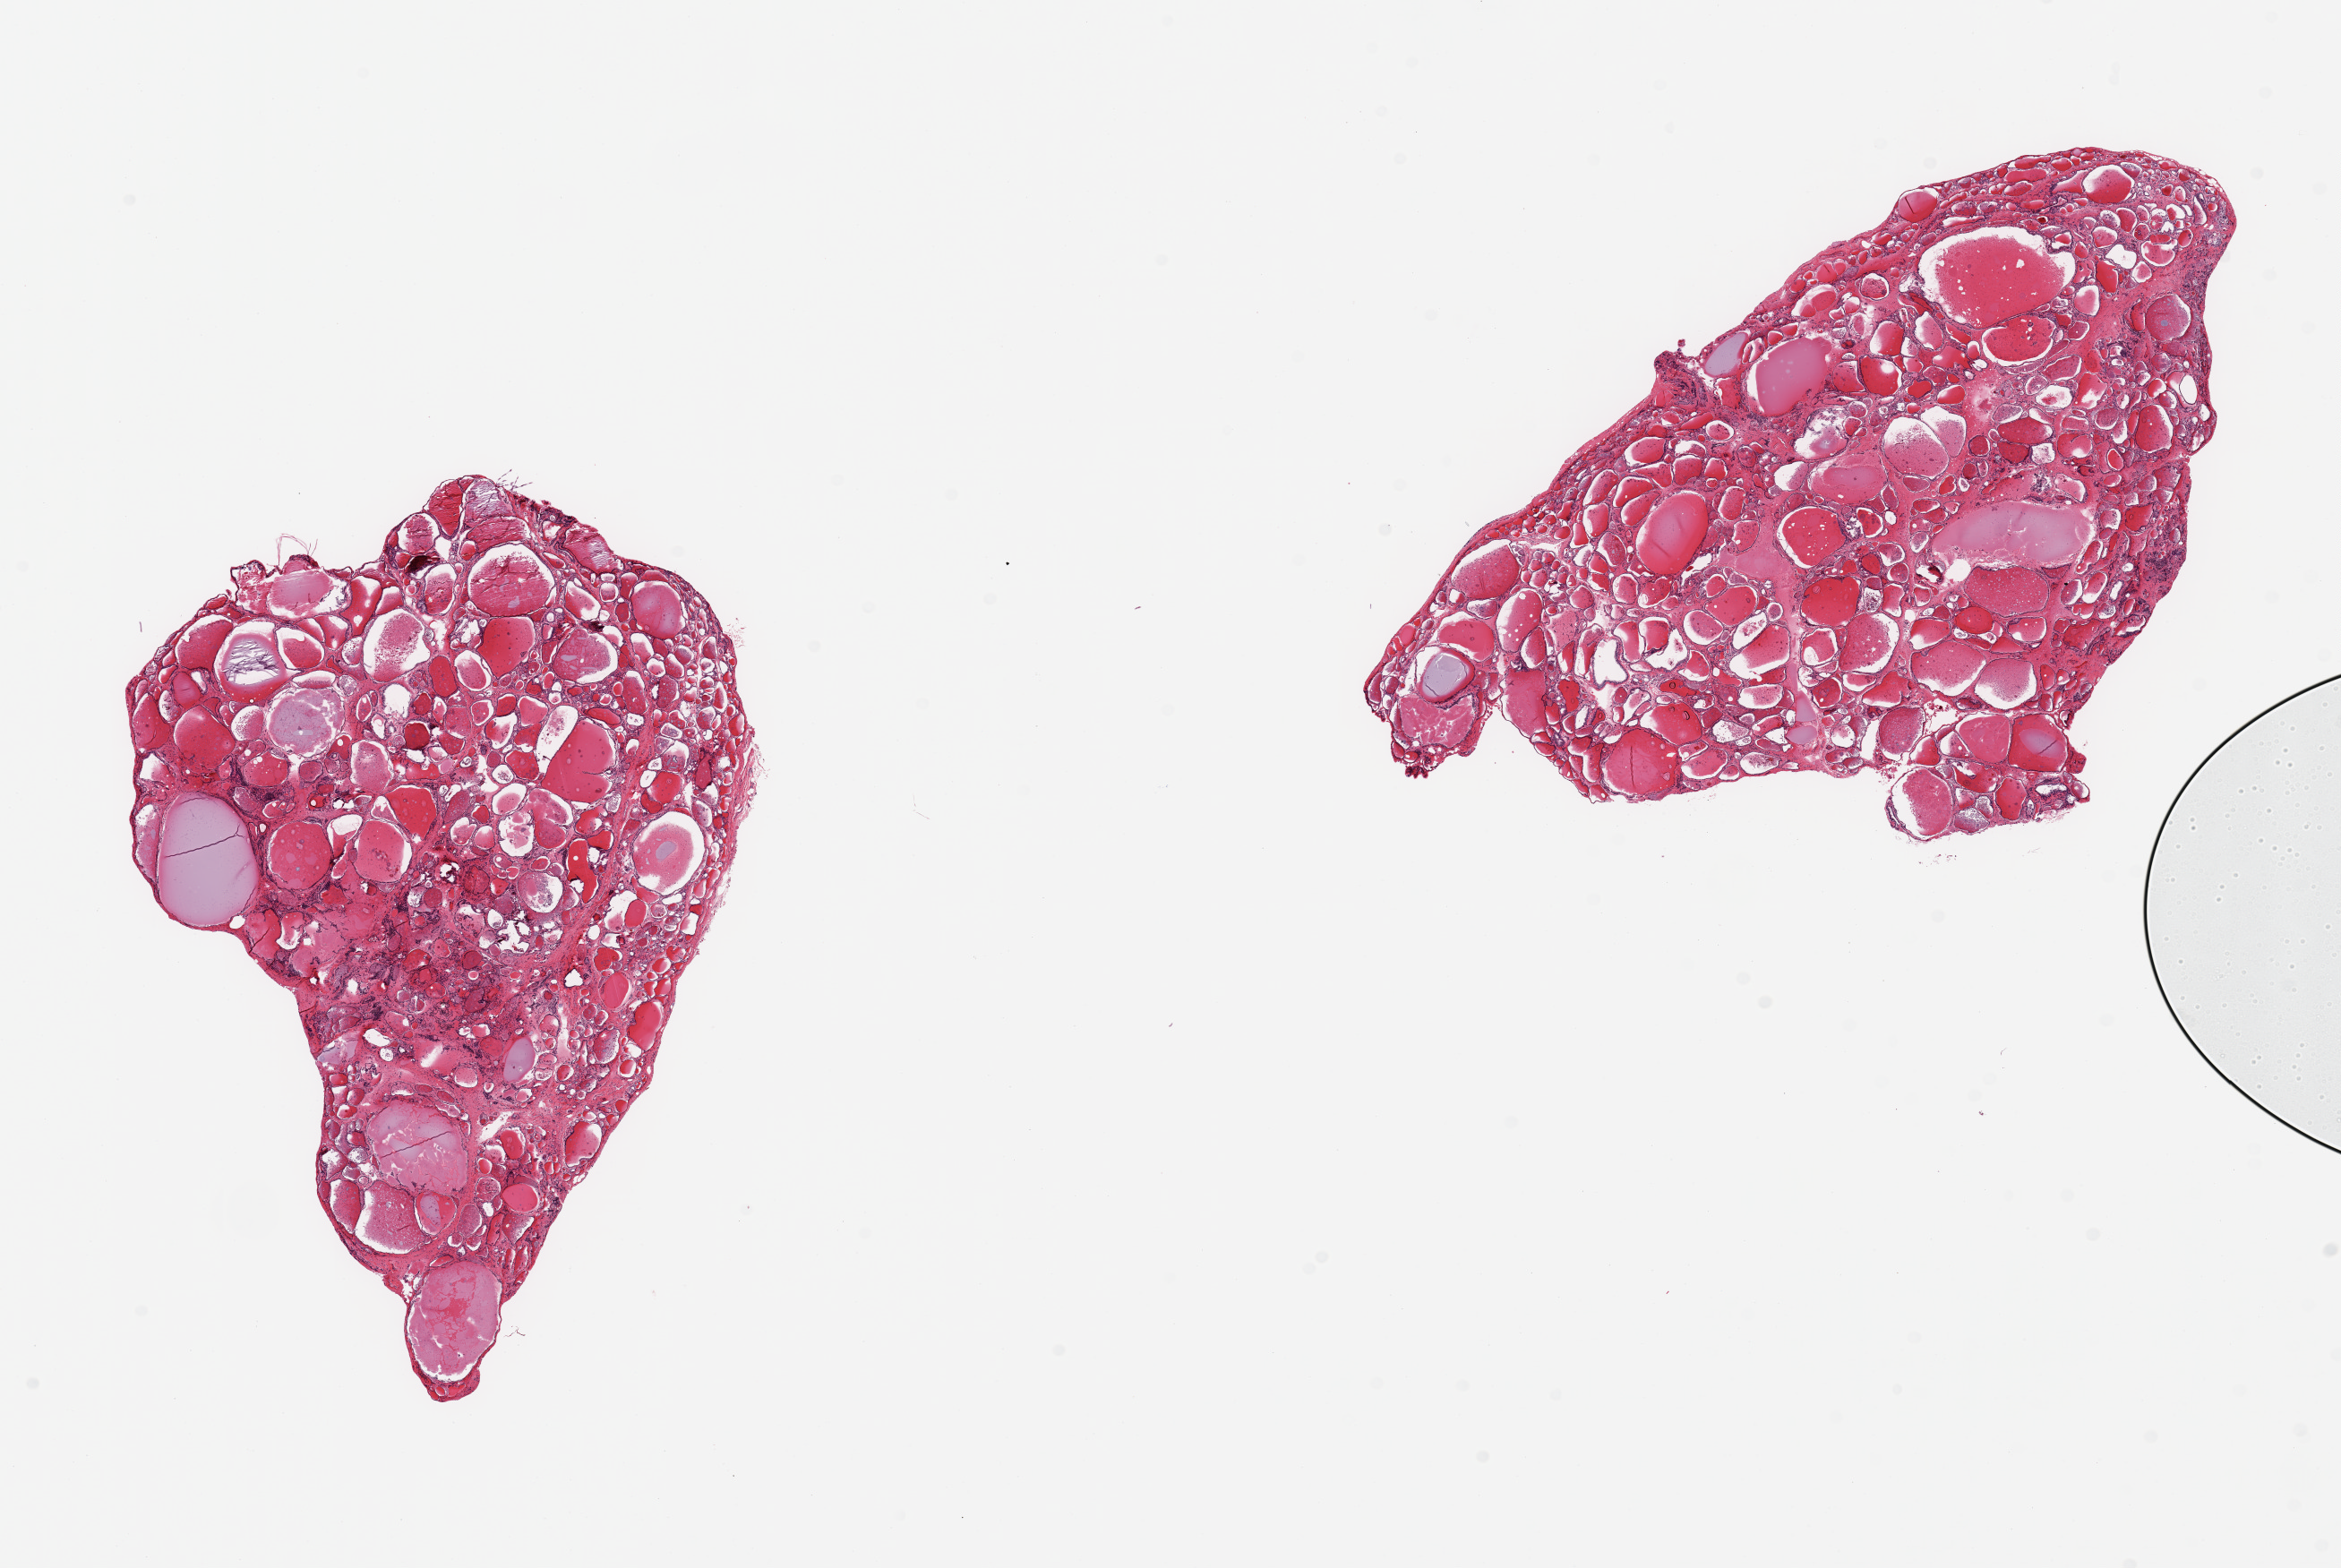
Whole-slide image, hematoxylin and eosin (H&E) stain, brightfield, whole scanned area (about 20.7 x 13.8 mm) shown as a low-resolution overview. PAXgene-fixed paraffin-embedded (PFPE) section. Target tissue: thyroid. Donor tissue sample. Donor: female.
Pathologist's review note for this sample: 2 pieces; multinodular goiter.